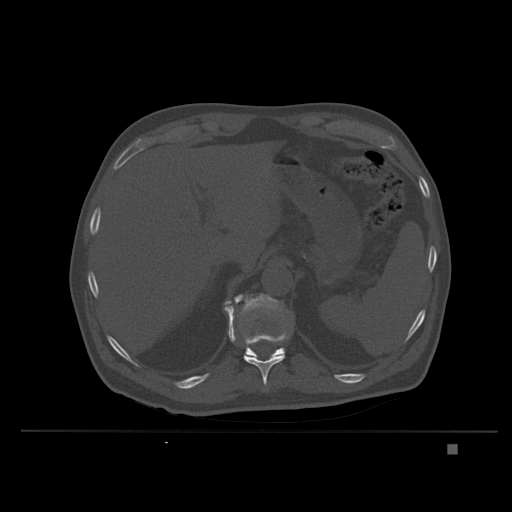
CT including the spine, one axial slice. Slice 171 of 435 in the series (ordered by position). Bone window (W 1800 / L 400 HU). 512 × 512 image matrix, field of view 434 × 434 mm. Male patient, age 73 years. Case-level facts recorded for this patient, not image findings: primary cancer: skin.
Structures marked on this image (semi-automatically segmented with operator editing):
- T11 vertebra: box from (x=226, y=307) to (x=290, y=391) px
- T12 vertebra: (x=224, y=294)–(x=287, y=358)